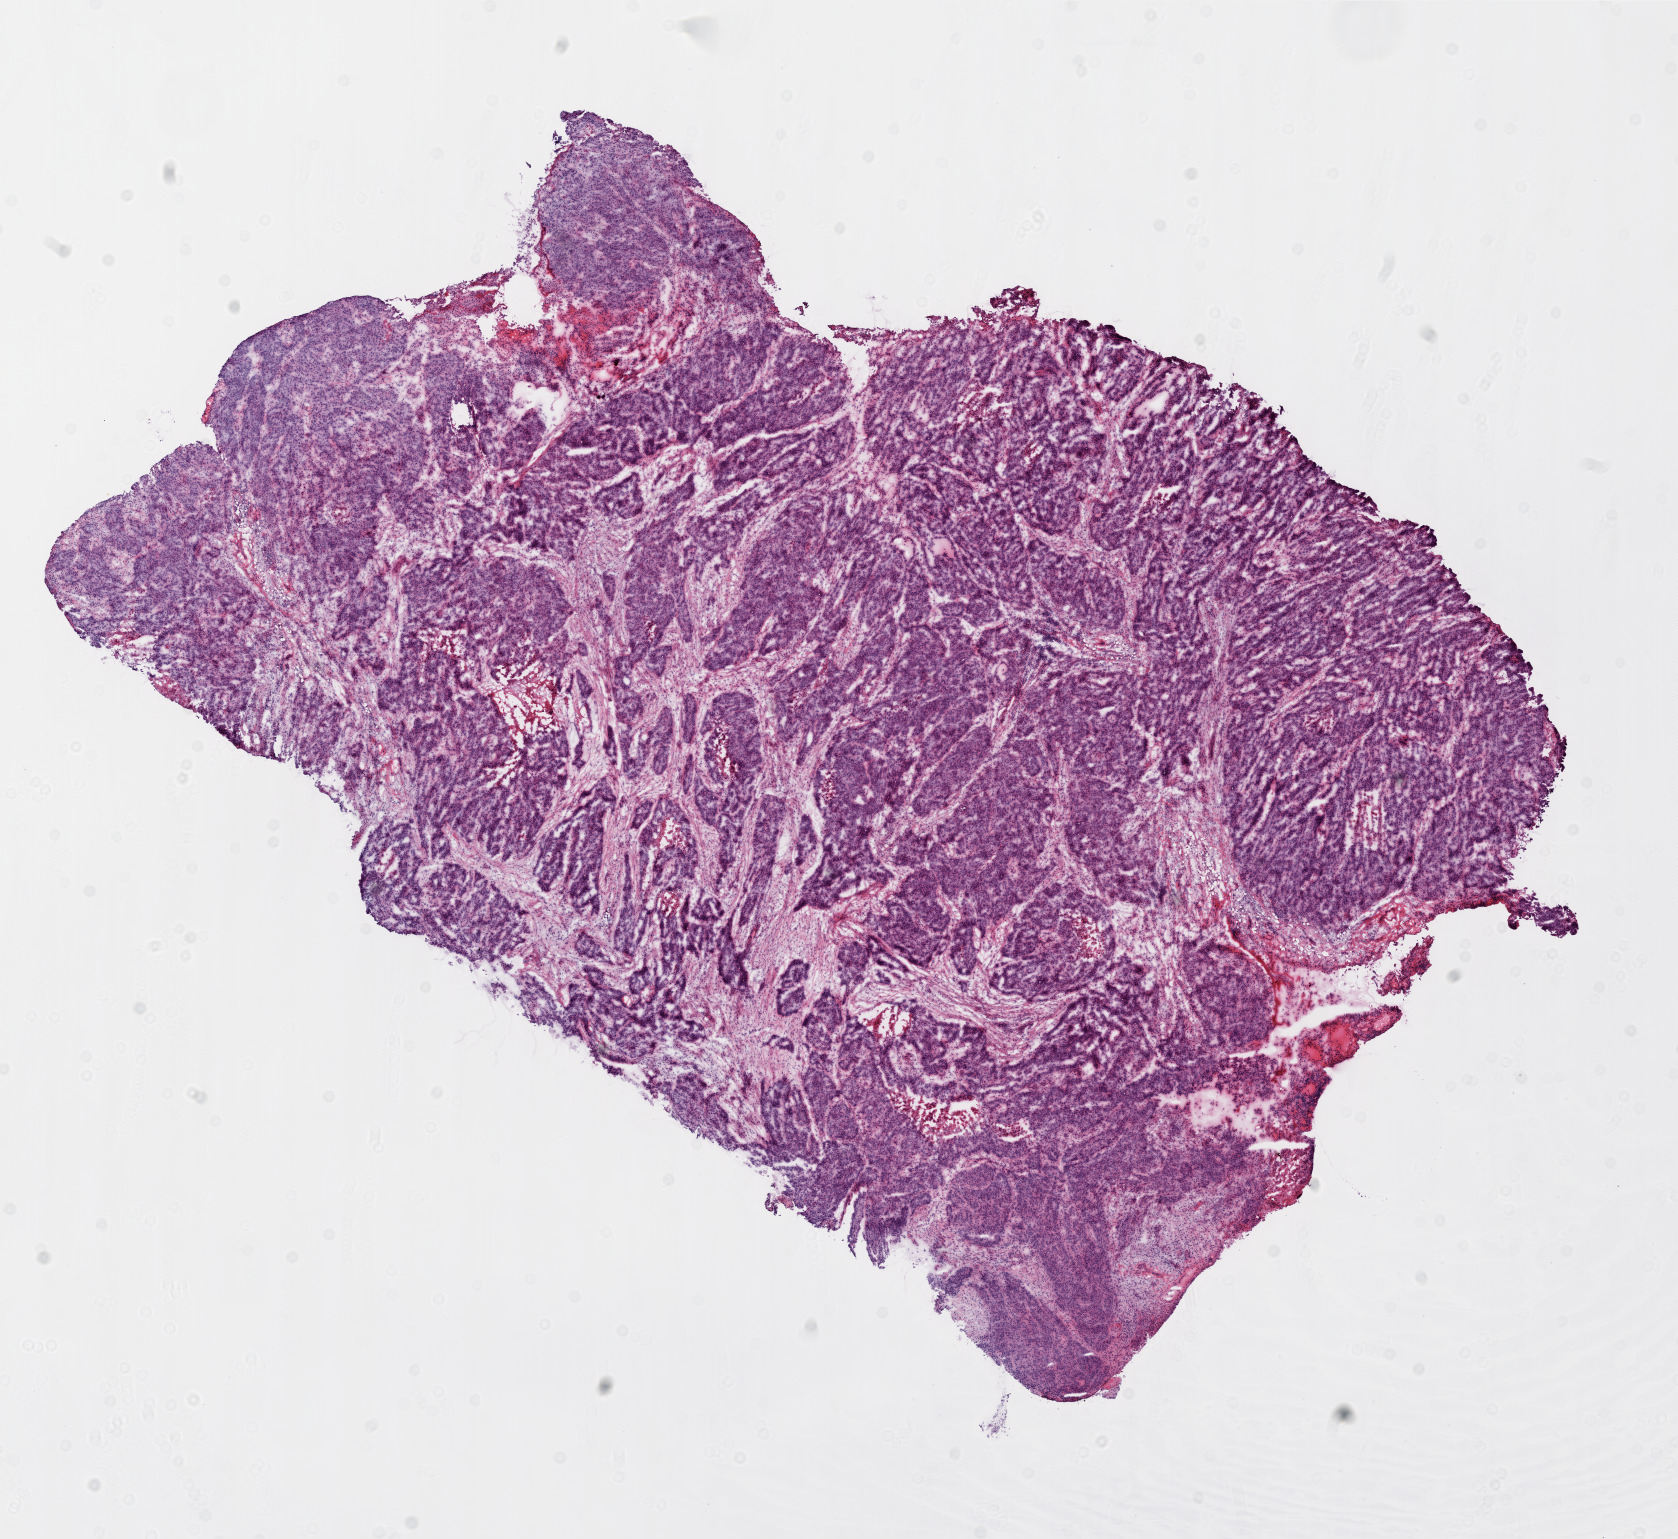
Whole-slide histology image, Hematoxylin and eosin (H&E) stained — low-resolution overview of the scanned area, about 13.5 x 12.4 mm; frozen section from the top of the tissue portion; primary tumour sample from the ovary. Female, age 57 years at initial diagnosis. Histologic grade: G3 (poorly differentiated). Composition of this section per pathologist review: tumour cells 85%, tumour nuclei 95%, normal cells 0%, stromal cells 15%, necrosis 0%.
Pathologic diagnosis: Serous cystadenocarcinoma, NOS. FIGO stage: IIIC. Laterality: bilateral.